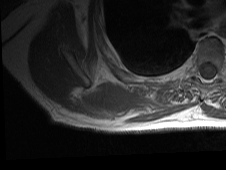
MRI of an extremity soft-tissue mass, one axial slice; slice 18 of 81 in the series (ordered by position); MR volume resampled by the dataset authors to the PET/CT grid (not the native acquisition matrix); 226 × 170 image matrix, field of view 221 × 166 mm. Male patient. From the clinical record (not read from this slice): histological type: pleiomorphic spindle cell undifferentiated; grade: high; site of the primary tumour: right parascapusular.
Structures marked on this image (expert contour drawn on MRI and transferred to this co-registered scan by the dataset authors):
- gross tumour volume including surrounding oedema: bounding box <60,83,189,123> (left, top, right, bottom; pixels)